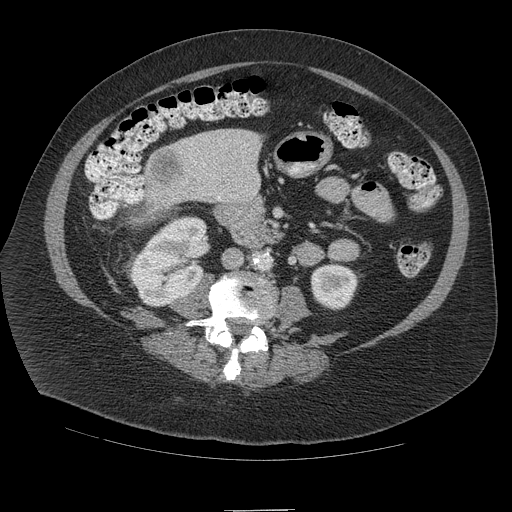
Contrast-enhanced abdominal CT (liver protocol), one axial slice; position 29 of 109 along the scan axis; reconstruction kernel STANDARD; 140 kVp; soft-tissue window (W 400 / L 40 HU); 512 × 512 image matrix, field of view 420 × 420 mm. From the clinical record (not read from this slice): diagnosis: hepatocellular carcinoma (patient treated with transarterial chemoembolisation; whether this scan precedes or follows treatment is not stated here); TNM stage (as recorded): Stage-IVB; Child-Pugh class: A; tumour nodularity: multinodular.
Annotated regions visible in this slice (semi-automatically segmented with operator editing):
- liver parenchyma outside the tumour (the mass and vessels are separate outlines, so this box may not span the whole liver): box from (x=176, y=128) to (x=262, y=206) px
- mass: (x=142, y=144)–(x=193, y=193)
- liver vessels: (x=194, y=161)–(x=255, y=200)